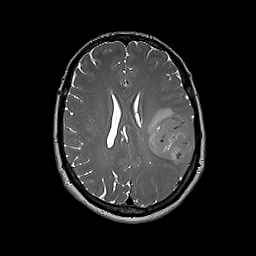
Brain MRI from a brain-tumour surgery series, one axial slice. Slice 84 of 192 in the series (ordered by position). 1 mm slice thickness. 256 × 256 image matrix, field of view 250 × 250 mm. From the clinical record (not read from this slice): histopathology: Glioblastoma; WHO grade: 4; IDH mutation: no; tumour location: Left Frontal.
Annotated regions visible in this slice (expert manual segmentation):
- tumour: bounding box <149,115,195,165> (left, top, right, bottom; pixels)